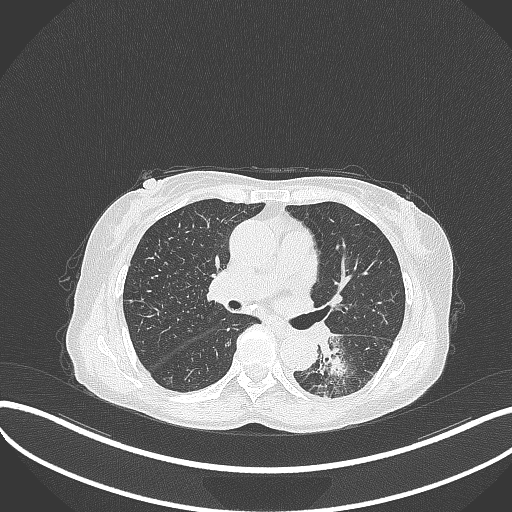
Chest CT, one axial slice; reconstruction kernel B70f; 120 kVp; lung window (W 1500 / L -600 HU); 1 mm slice thickness; 512 × 512 image matrix, field of view 400 × 400 mm. Female patient, age 78 years. From the clinical record (not read from this slice): clinical TNM (as recorded): T3 N0 M1.
Outlined on this slice (bounding box drawn by a radiologist):
- lung tumour (recorded histology: squamous cell carcinoma): bounding box [x1, y1, x2, y2] px = [314, 333, 360, 389]